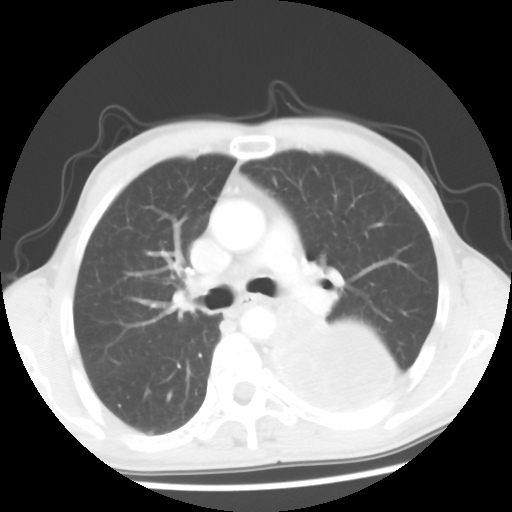
Chest CT, one axial slice; position 36 of 56 along the scan axis; lung window (W 1500 / L -600 HU); 5 mm slice thickness; 512 × 512 image matrix, field of view 318 × 318 mm. Patient: male, 60 years. Case-level facts recorded for this patient, not image findings: clinical TNM (as recorded): T4 N0 M0.
Outlined on this slice (rectangle marked by the reading radiologist):
- lung tumour (recorded histology: squamous cell carcinoma): bounding box [x1, y1, x2, y2] px = [271, 301, 435, 423]